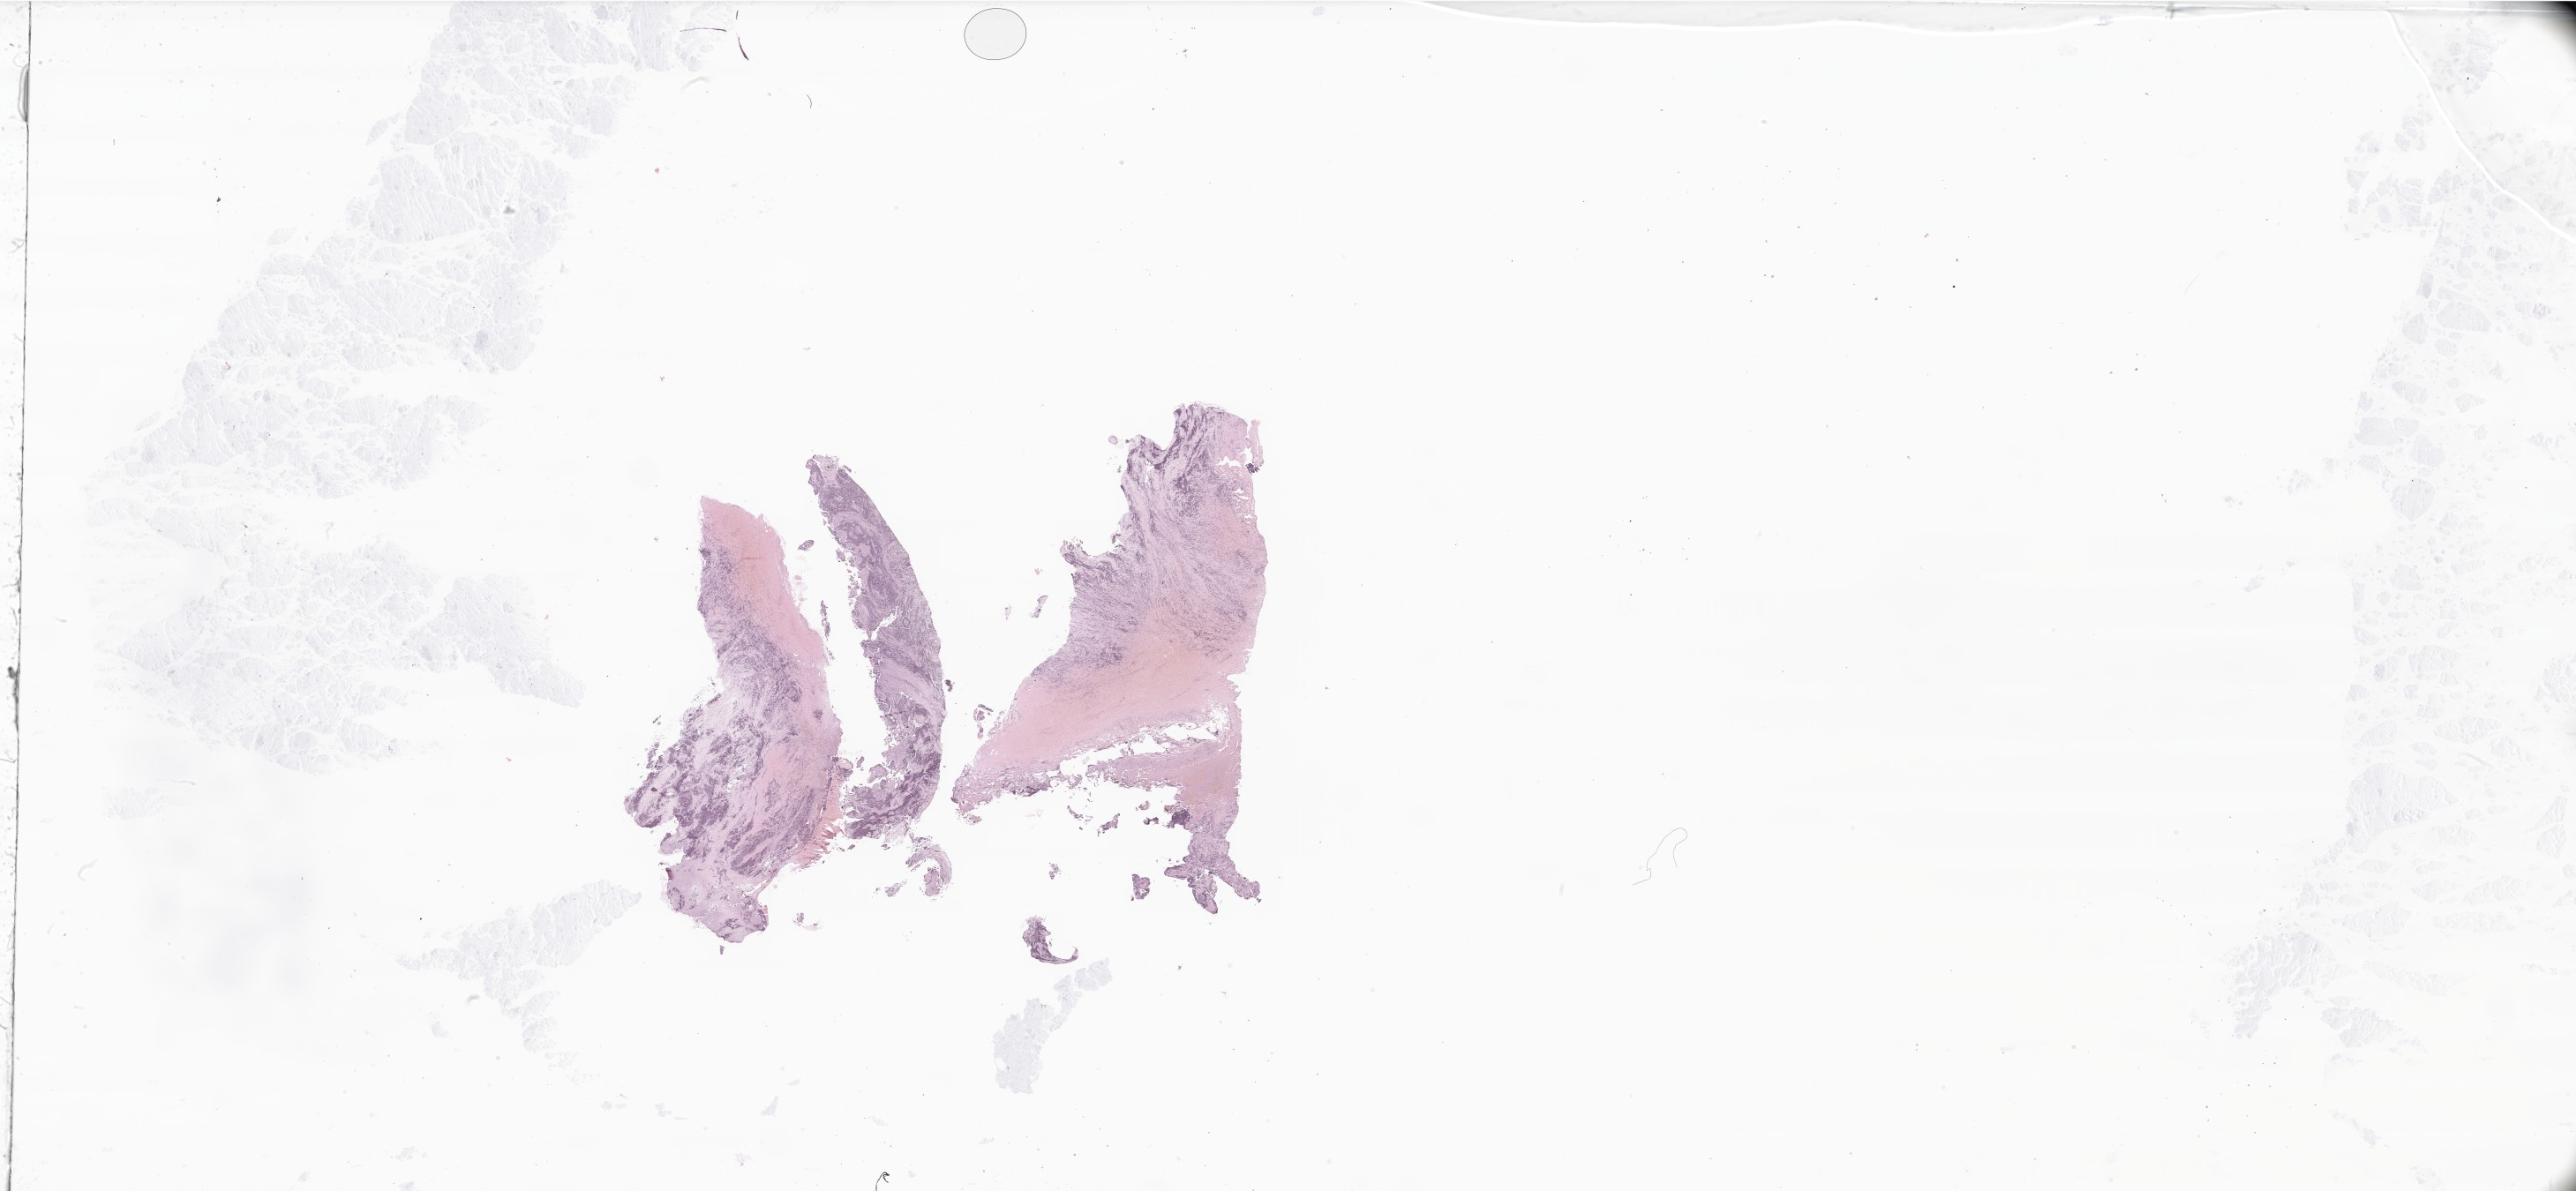
Whole-slide image, hematoxylin and eosin (H&E) stain of tumor tissue from the retroperitoneum, whole scanned area (about 49.2 x 22.8 mm) shown as a low-resolution overview. Formalin-fixed, paraffin-embedded (FFPE) tissue. Male patient, age 847 days.
Recorded diagnosis: Neuroblastoma, NOS.